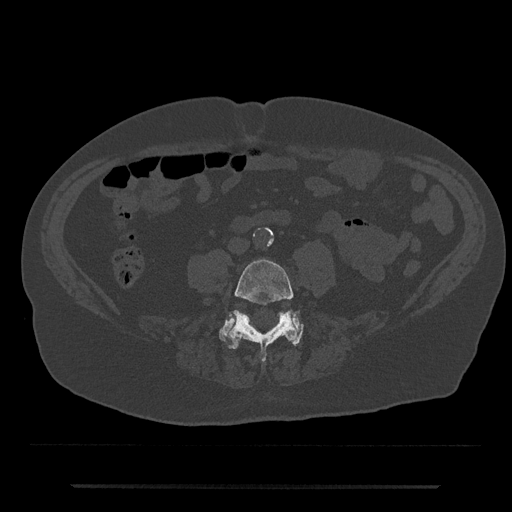
CT including the spine, one axial slice. Position 340 of 797 along the scan axis. Reconstruction kernel Br40s/3. Bone window (W 1800 / L 400 HU). 0.5 mm slice thickness. 512 × 512 image matrix. Male patient, age 80 years. From the clinical record (not read from this slice): primary cancer: prostate.
Outlined on this slice (semi-automatic segmentation, software-assisted and operator-edited):
- L4 vertebra: bounding box <229,259,298,362> (left, top, right, bottom; pixels)
- L5 vertebra: <219,312,303,346>